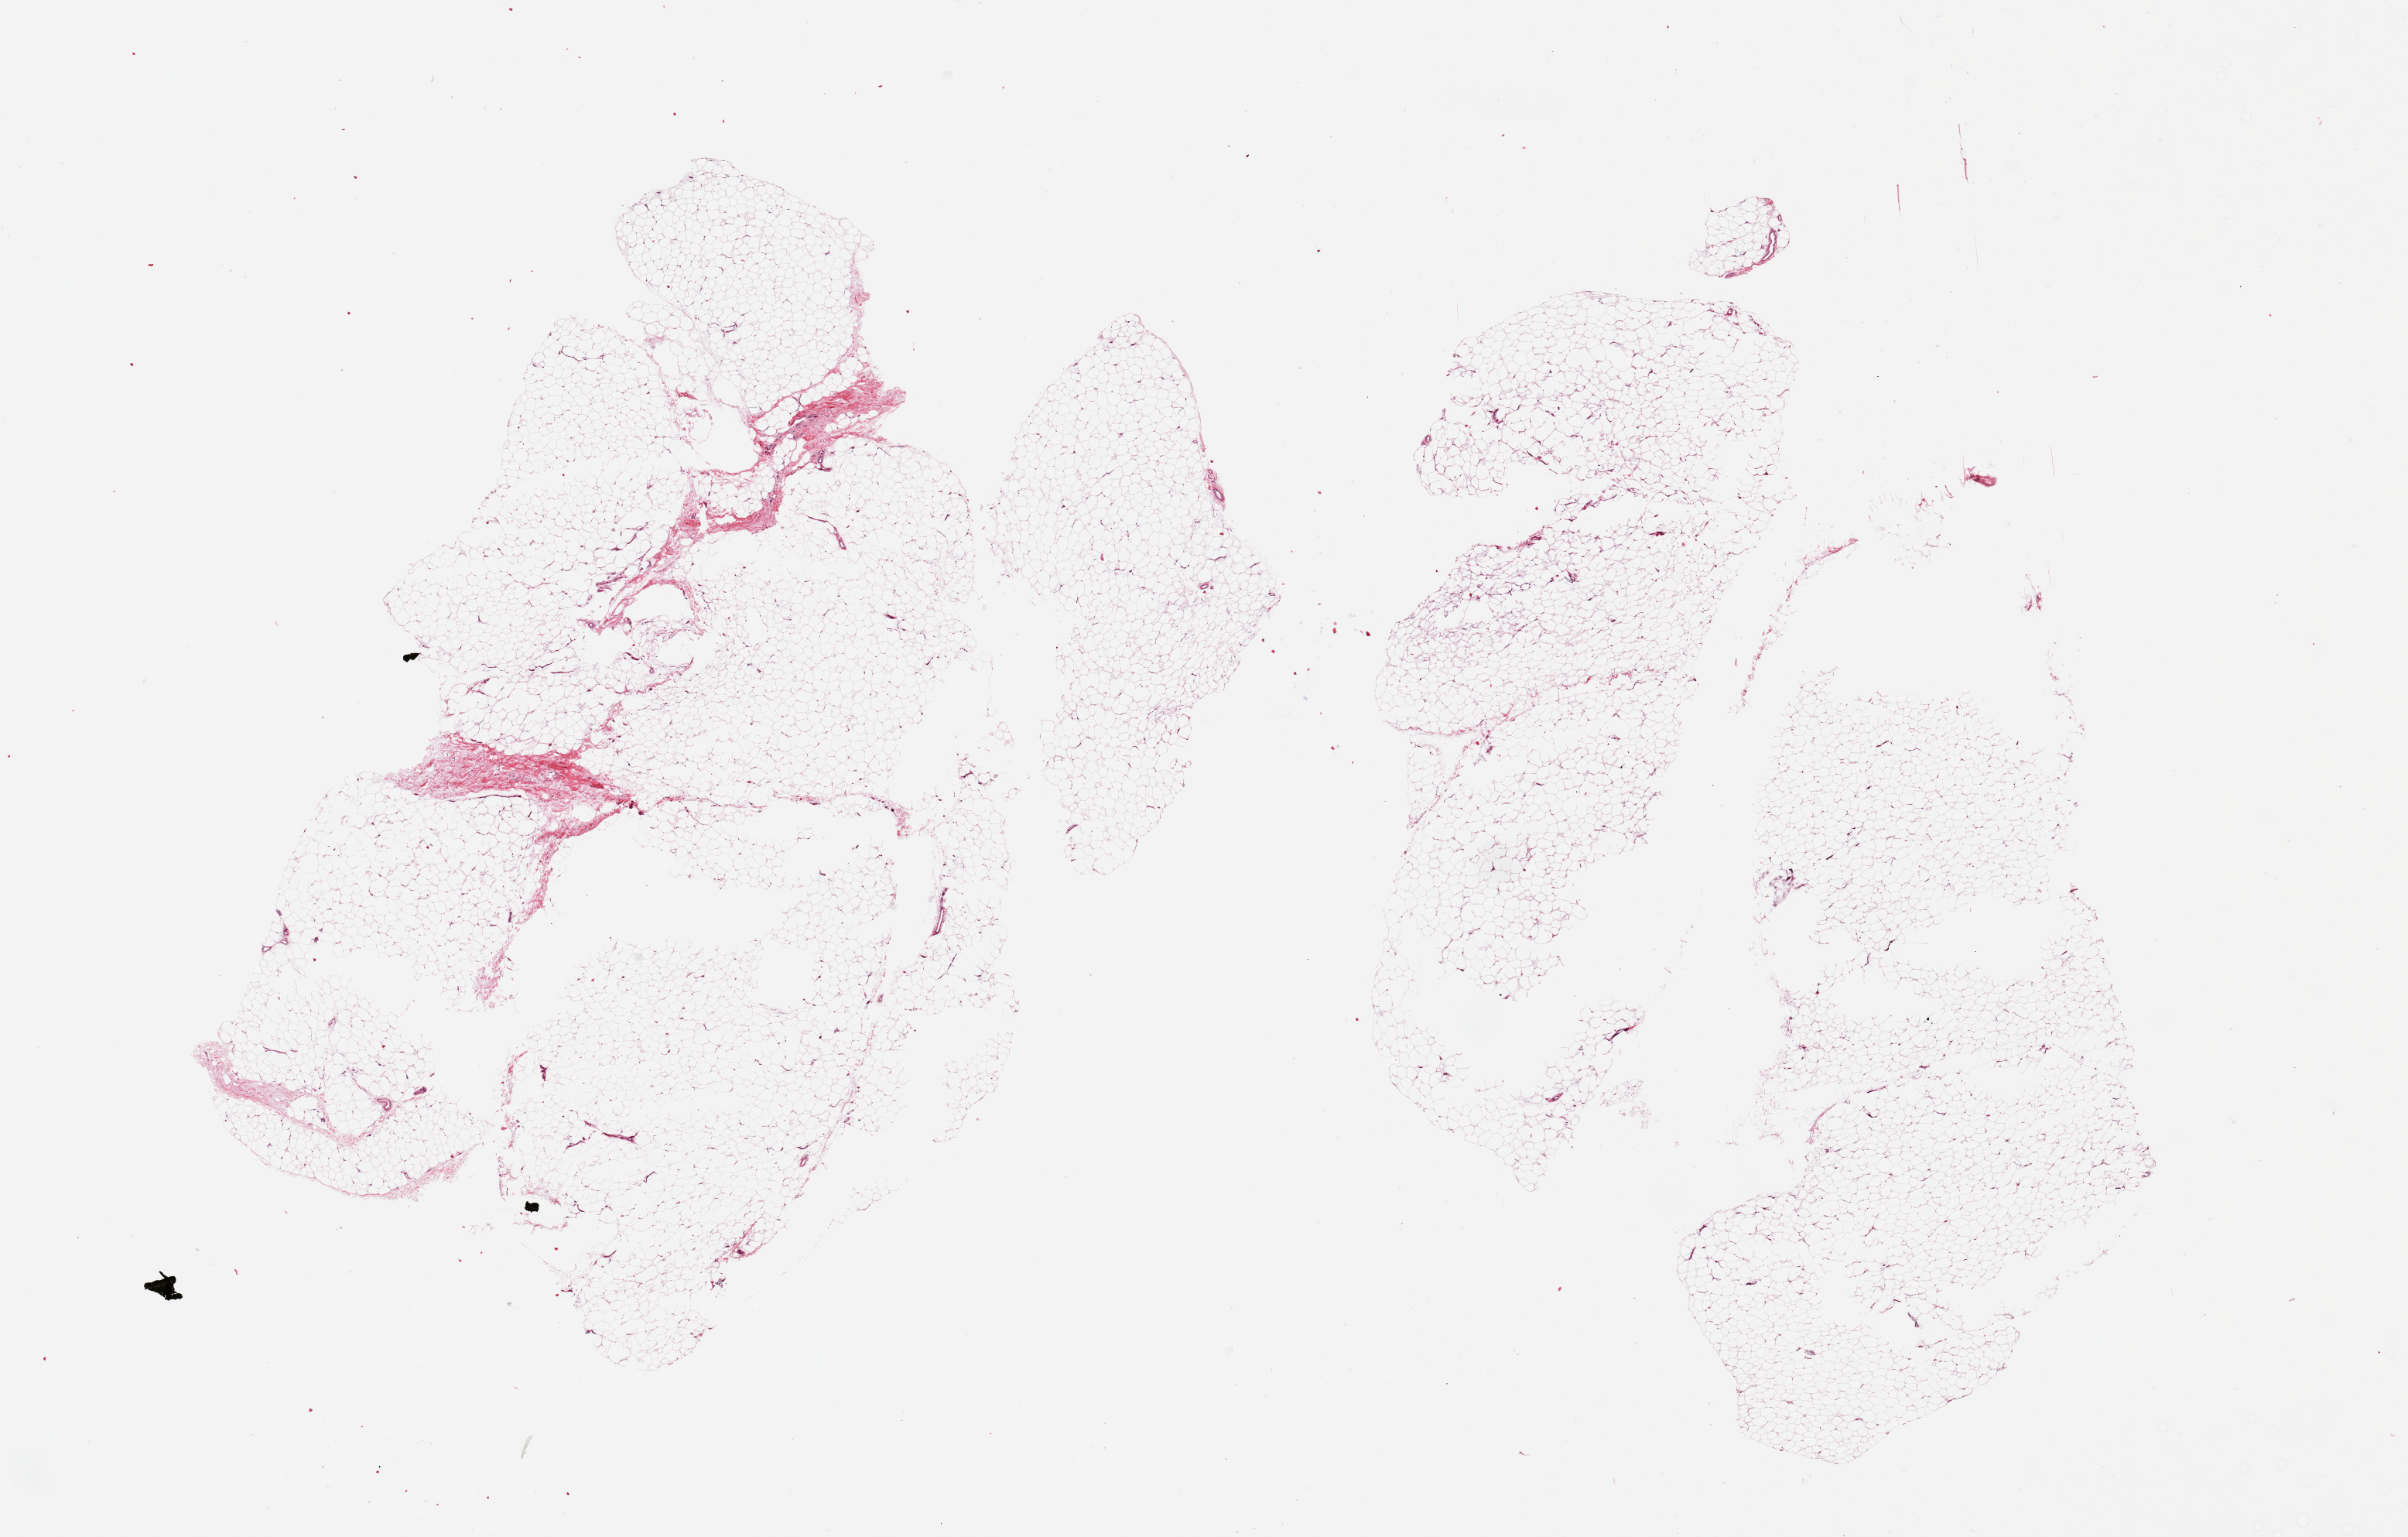
Digitized haematoxylin and eosin-stained section, brightfield — shown as a low-resolution overview of the whole scanned area (about 24.6 x 15.7 mm); PAXgene-fixed paraffin-embedded (PFPE) section; sampled site (target tissue): adipose tissue; donor tissue sample. Donor: female.
• review note (as recorded): 2 pieces; fat with minimal fibrous stroma